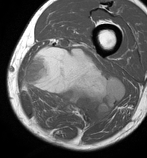
MRI of an extremity soft-tissue mass, one axial slice; position 37 of 86 along the scan axis; MR volume resampled by the dataset authors to the PET/CT grid (not the native acquisition matrix); 147 × 158 image matrix. Male patient. Case-level facts recorded for this patient, not image findings: histological type: undifferentiated pleomorphic liposarcoma; grade: high; site of the primary tumour: left thigh.
Outlined on this slice (expert contour drawn on MRI and transferred to this co-registered scan by the dataset authors):
- gross tumour volume including surrounding oedema: bounding box <23,44,125,127> (left, top, right, bottom; pixels)
- gross tumour volume (mass): <23,46,125,127>